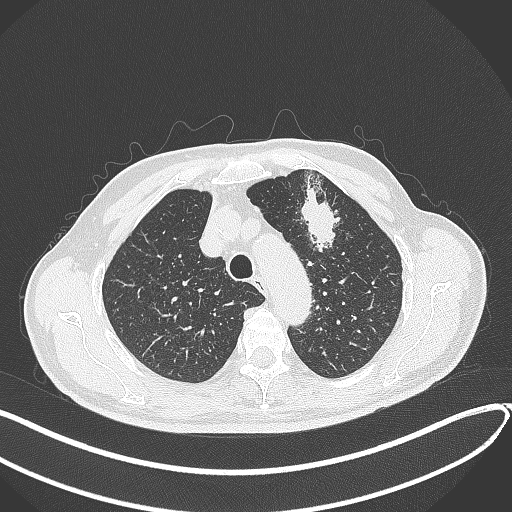
Chest CT, one axial slice; reconstruction kernel B70f; 120 kVp; lung window (W 1500 / L -600 HU); 512 × 512 image matrix, field of view 400 × 400 mm. Male patient, age 74 years. Case-level facts recorded for this patient, not image findings: clinical TNM (as recorded): T2b N0 M1c.
Annotated regions visible in this slice (rectangle marked by the reading radiologist):
- lung tumour (recorded histology: adenocarcinoma): box from (x=296, y=183) to (x=344, y=255) px